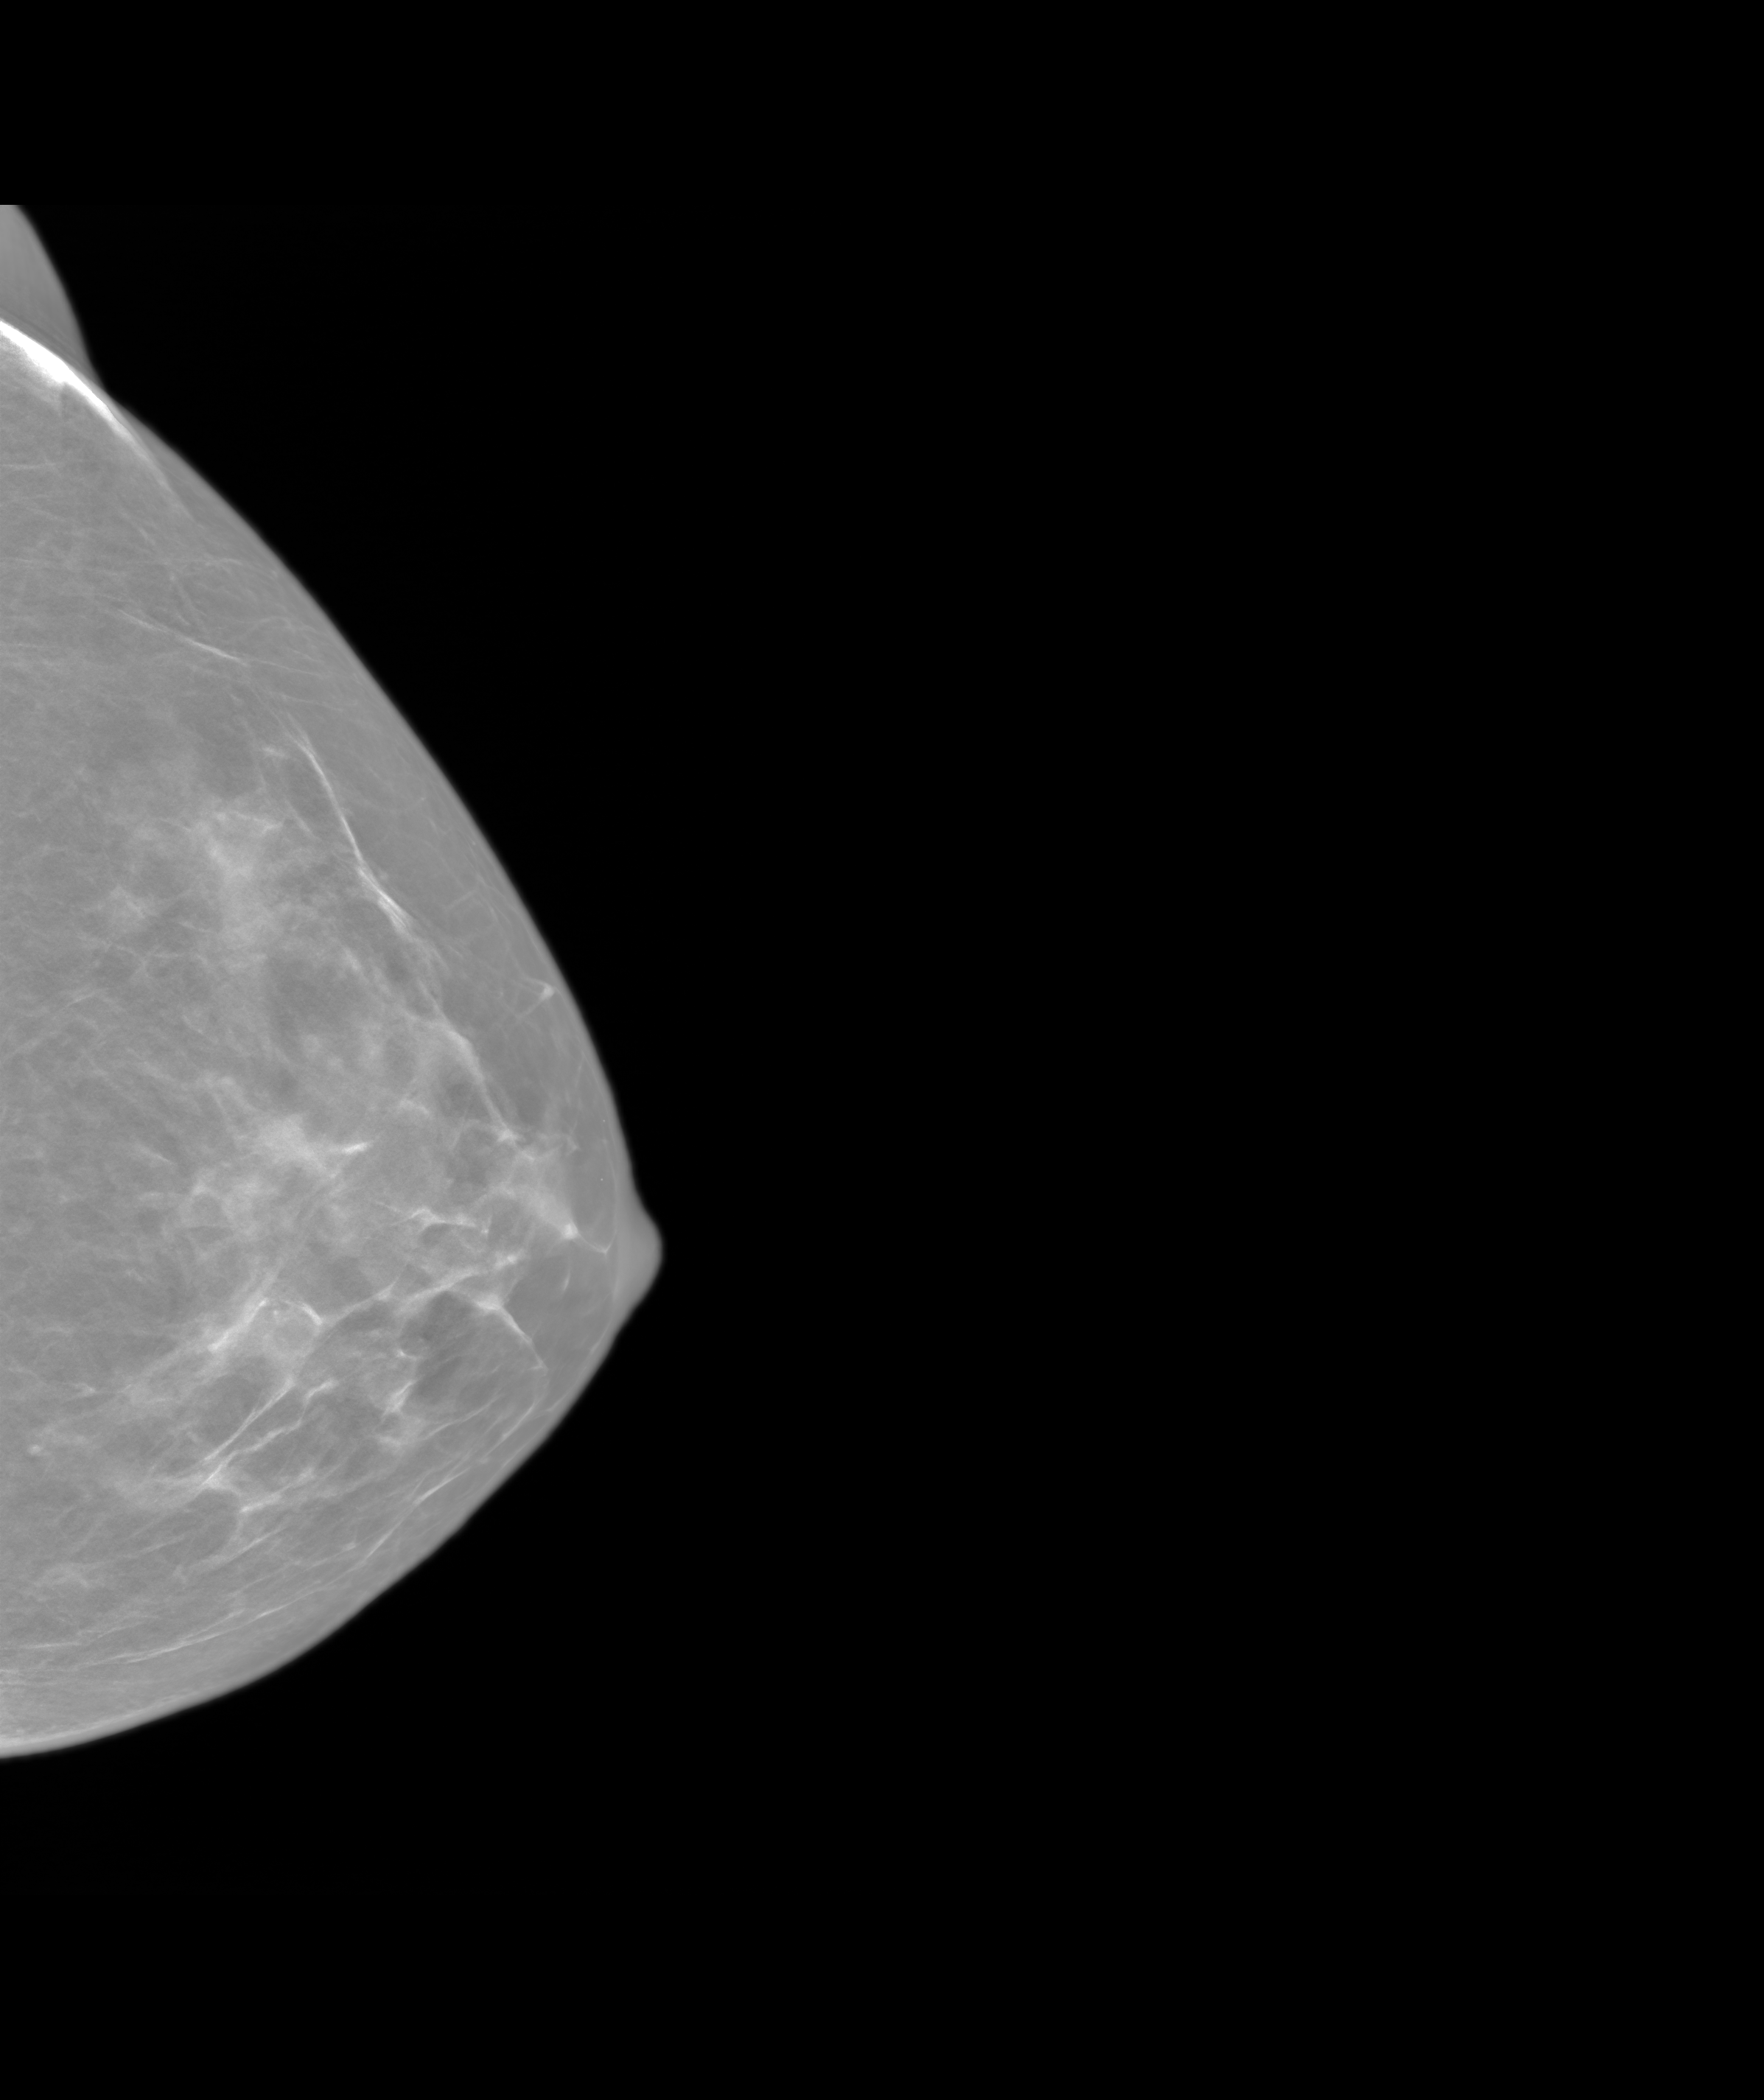
Screening examination. Patient aged 44 years (female).
Image type: synthesized 2-D view from tomosynthesis. Breast: left. Projection: CC view.